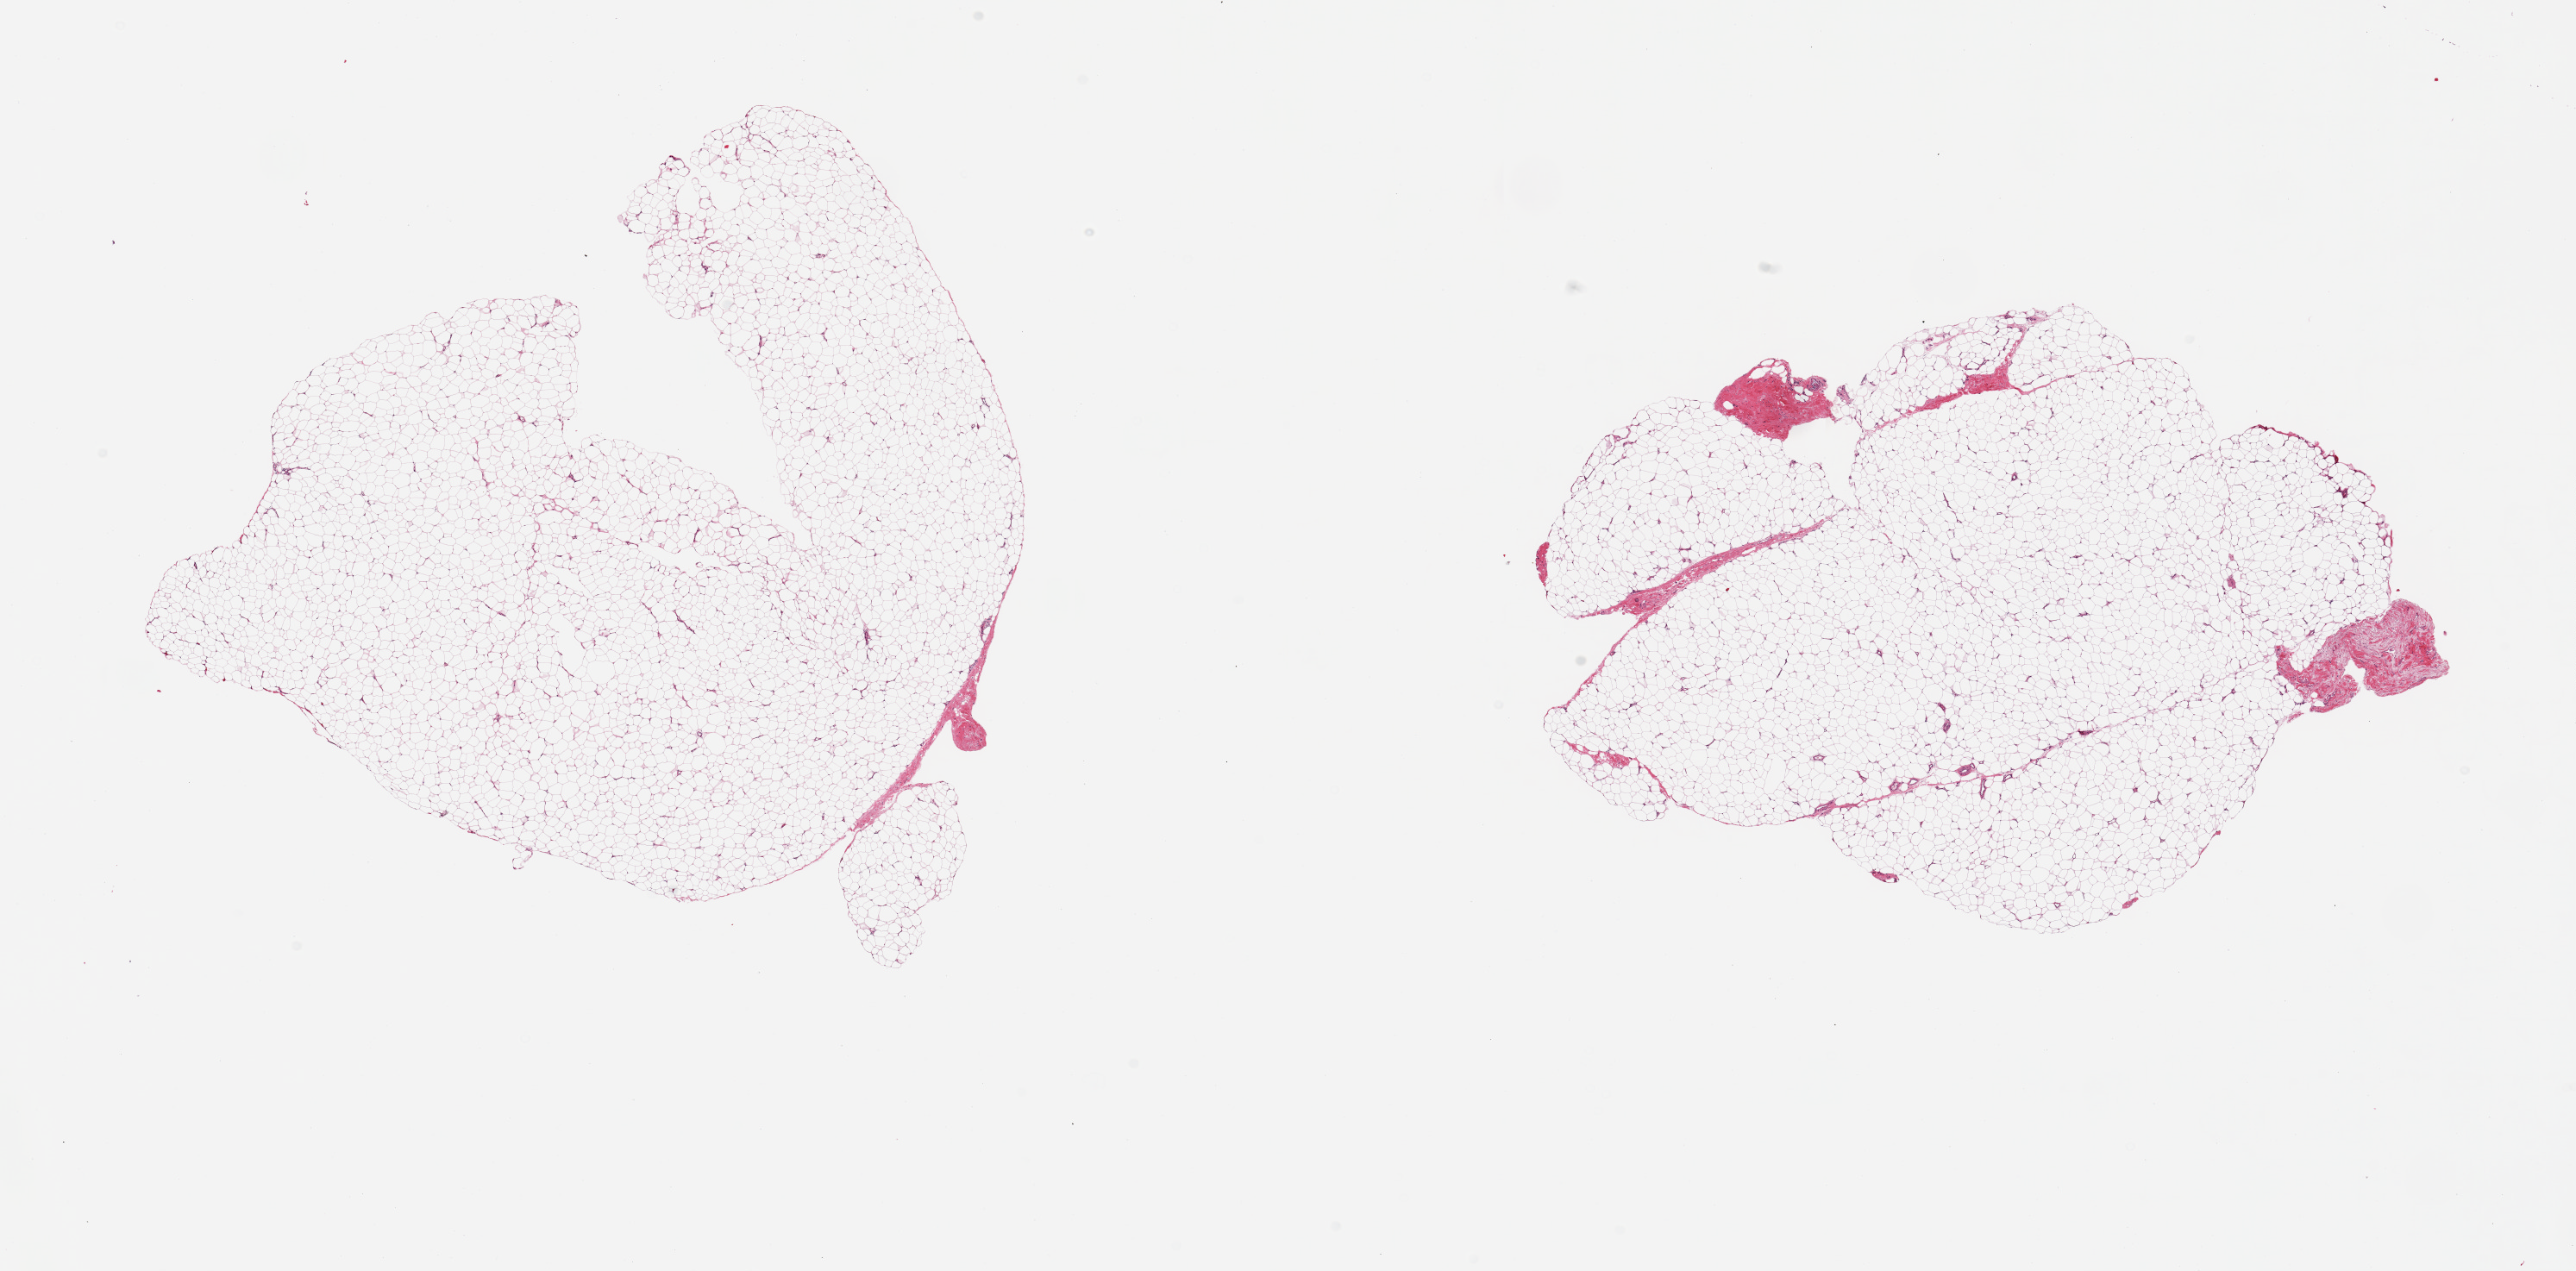
Haematoxylin and eosin whole-slide image, brightfield, a low-resolution overview of the entire scanned area, about 23.6 x 11.7 mm; PAXgene-fixed, paraffin-embedded tissue; sampled site (target tissue): adipose tissue; donor tissue sample. Donor sex: female.
Review note (as recorded): 2 pieces; 5% fibrous content mainly on the edges.